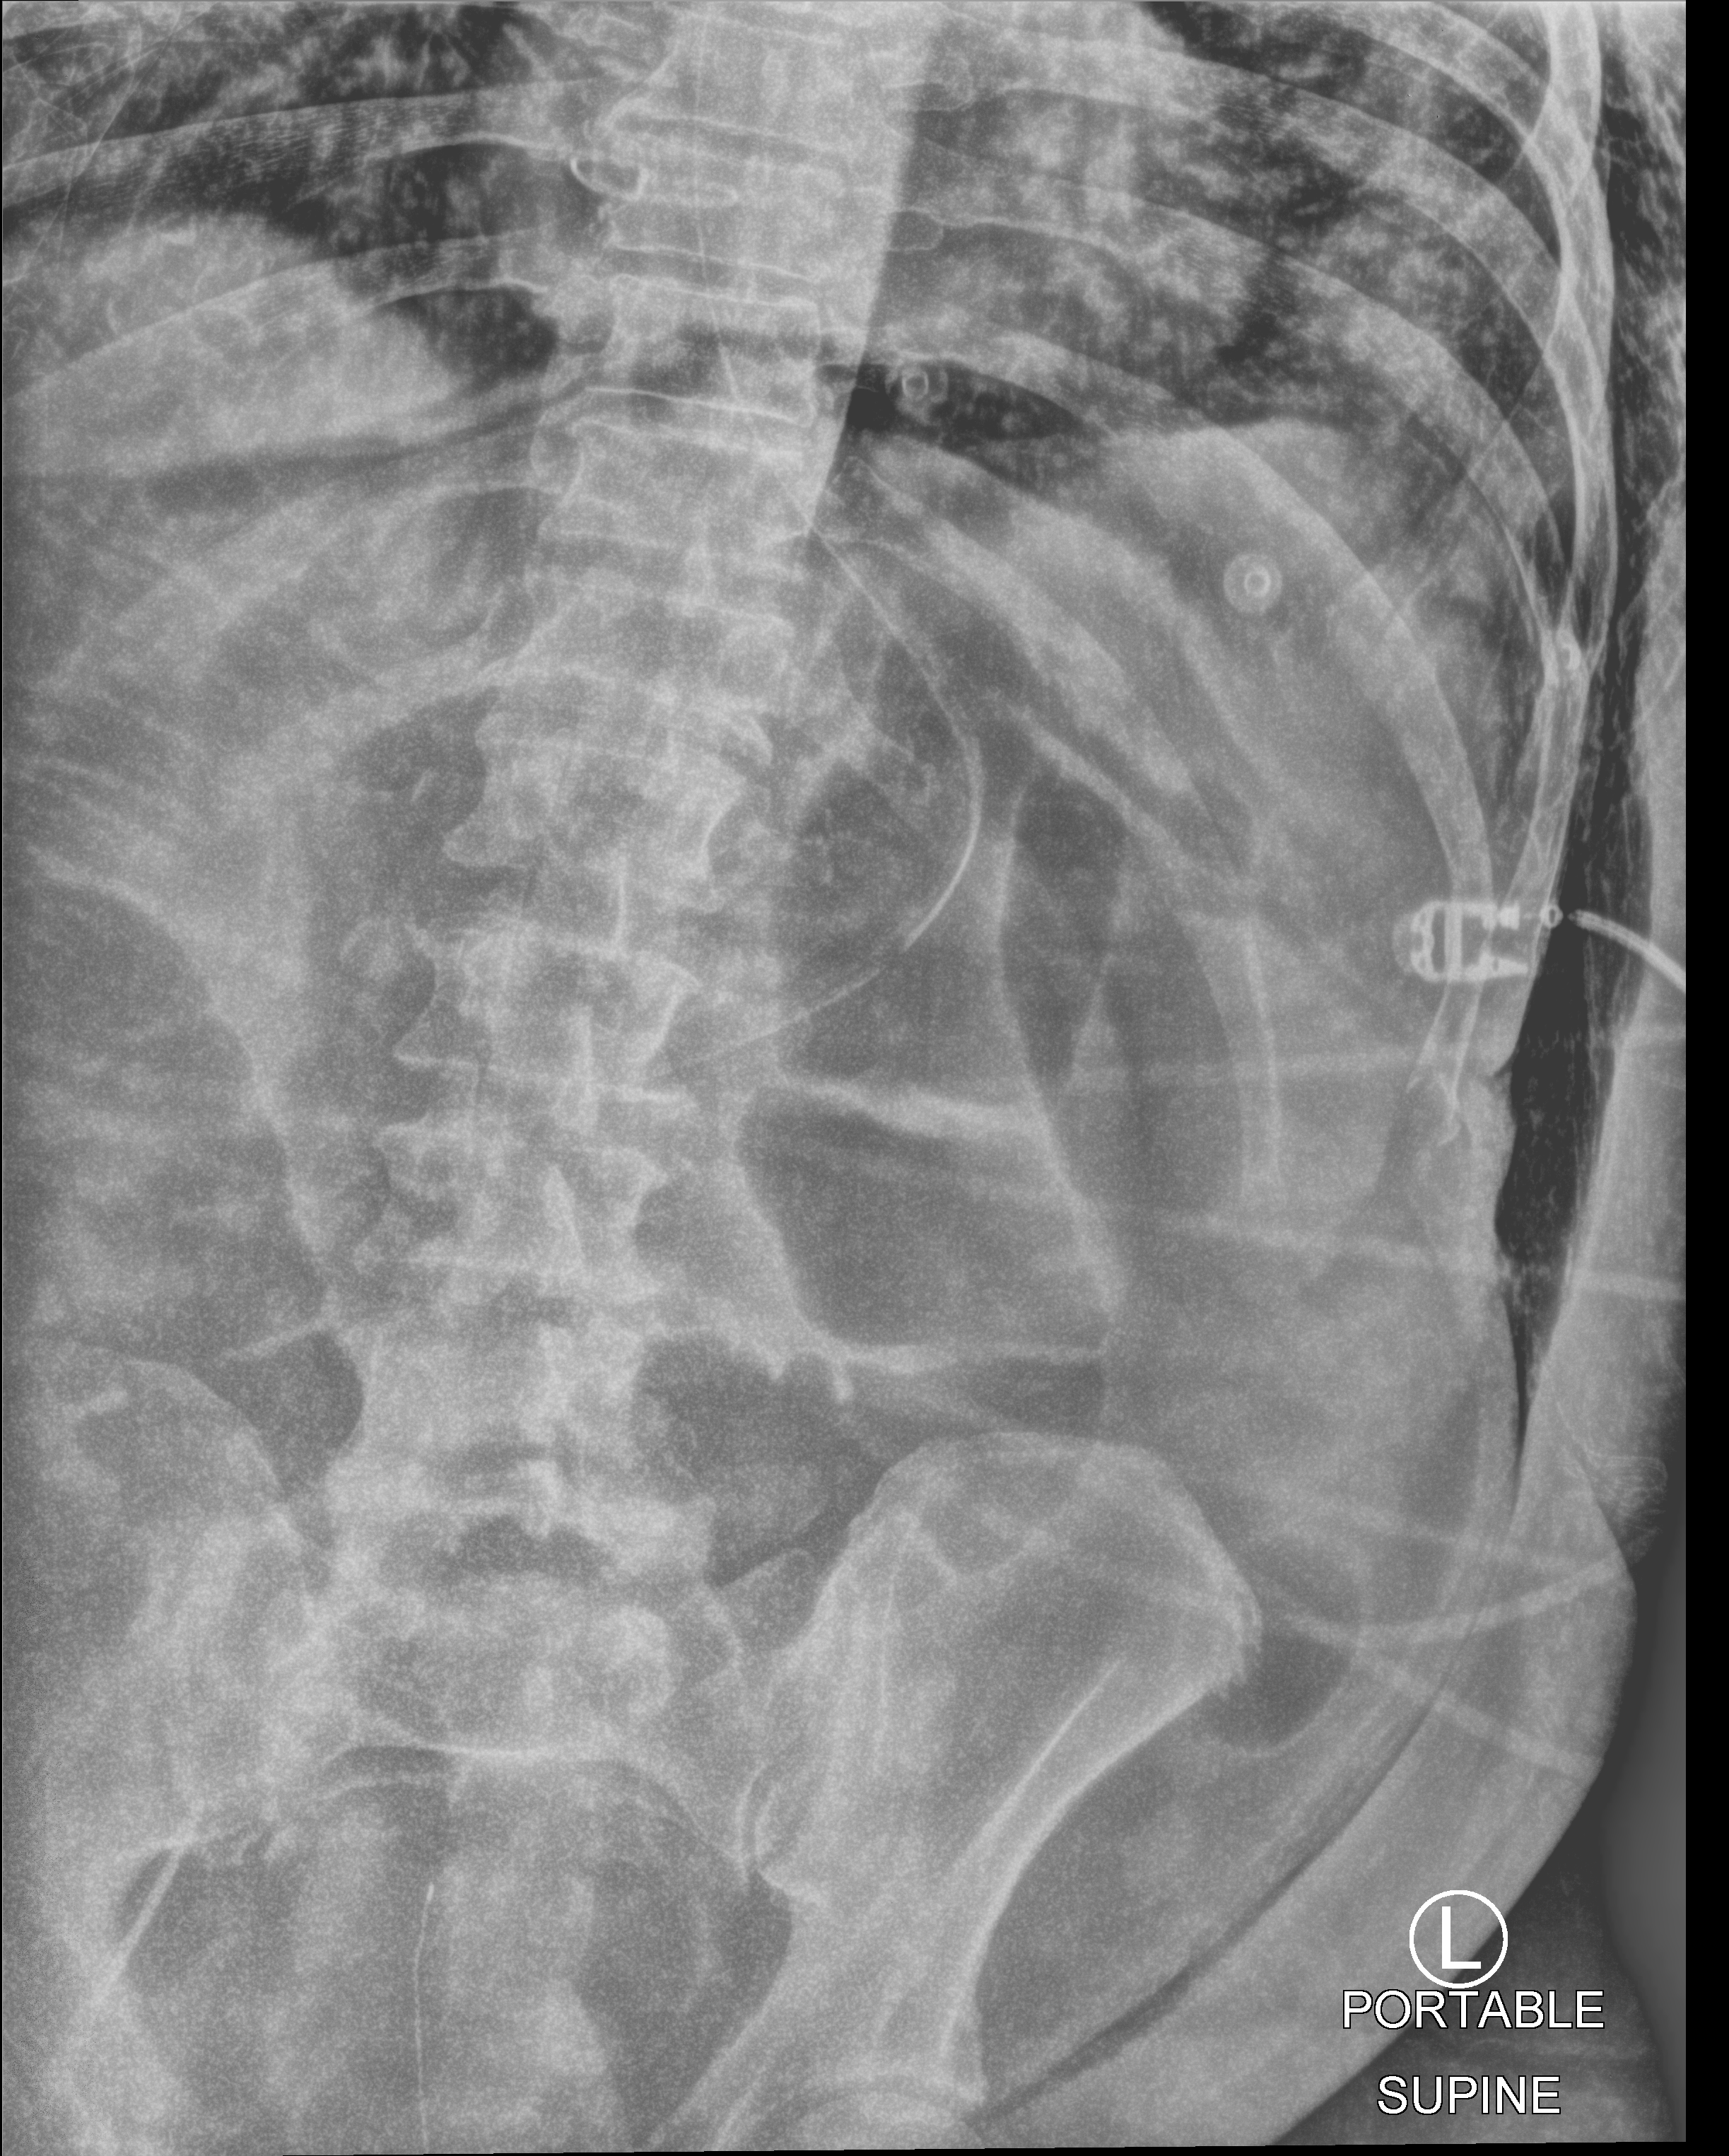
Bedside abdomen radiograph (computed radiography); anteroposterior (AP) projection. Male patient hospitalised with COVID-19, age 60–74 years.
Admission-level facts for this patient (not findings on this image; timing relative to this image not recorded):
- mechanically ventilated during this hospital stay: yes
- length of hospital stay: 44 days
- admitted to intensive care during this hospital stay: yes